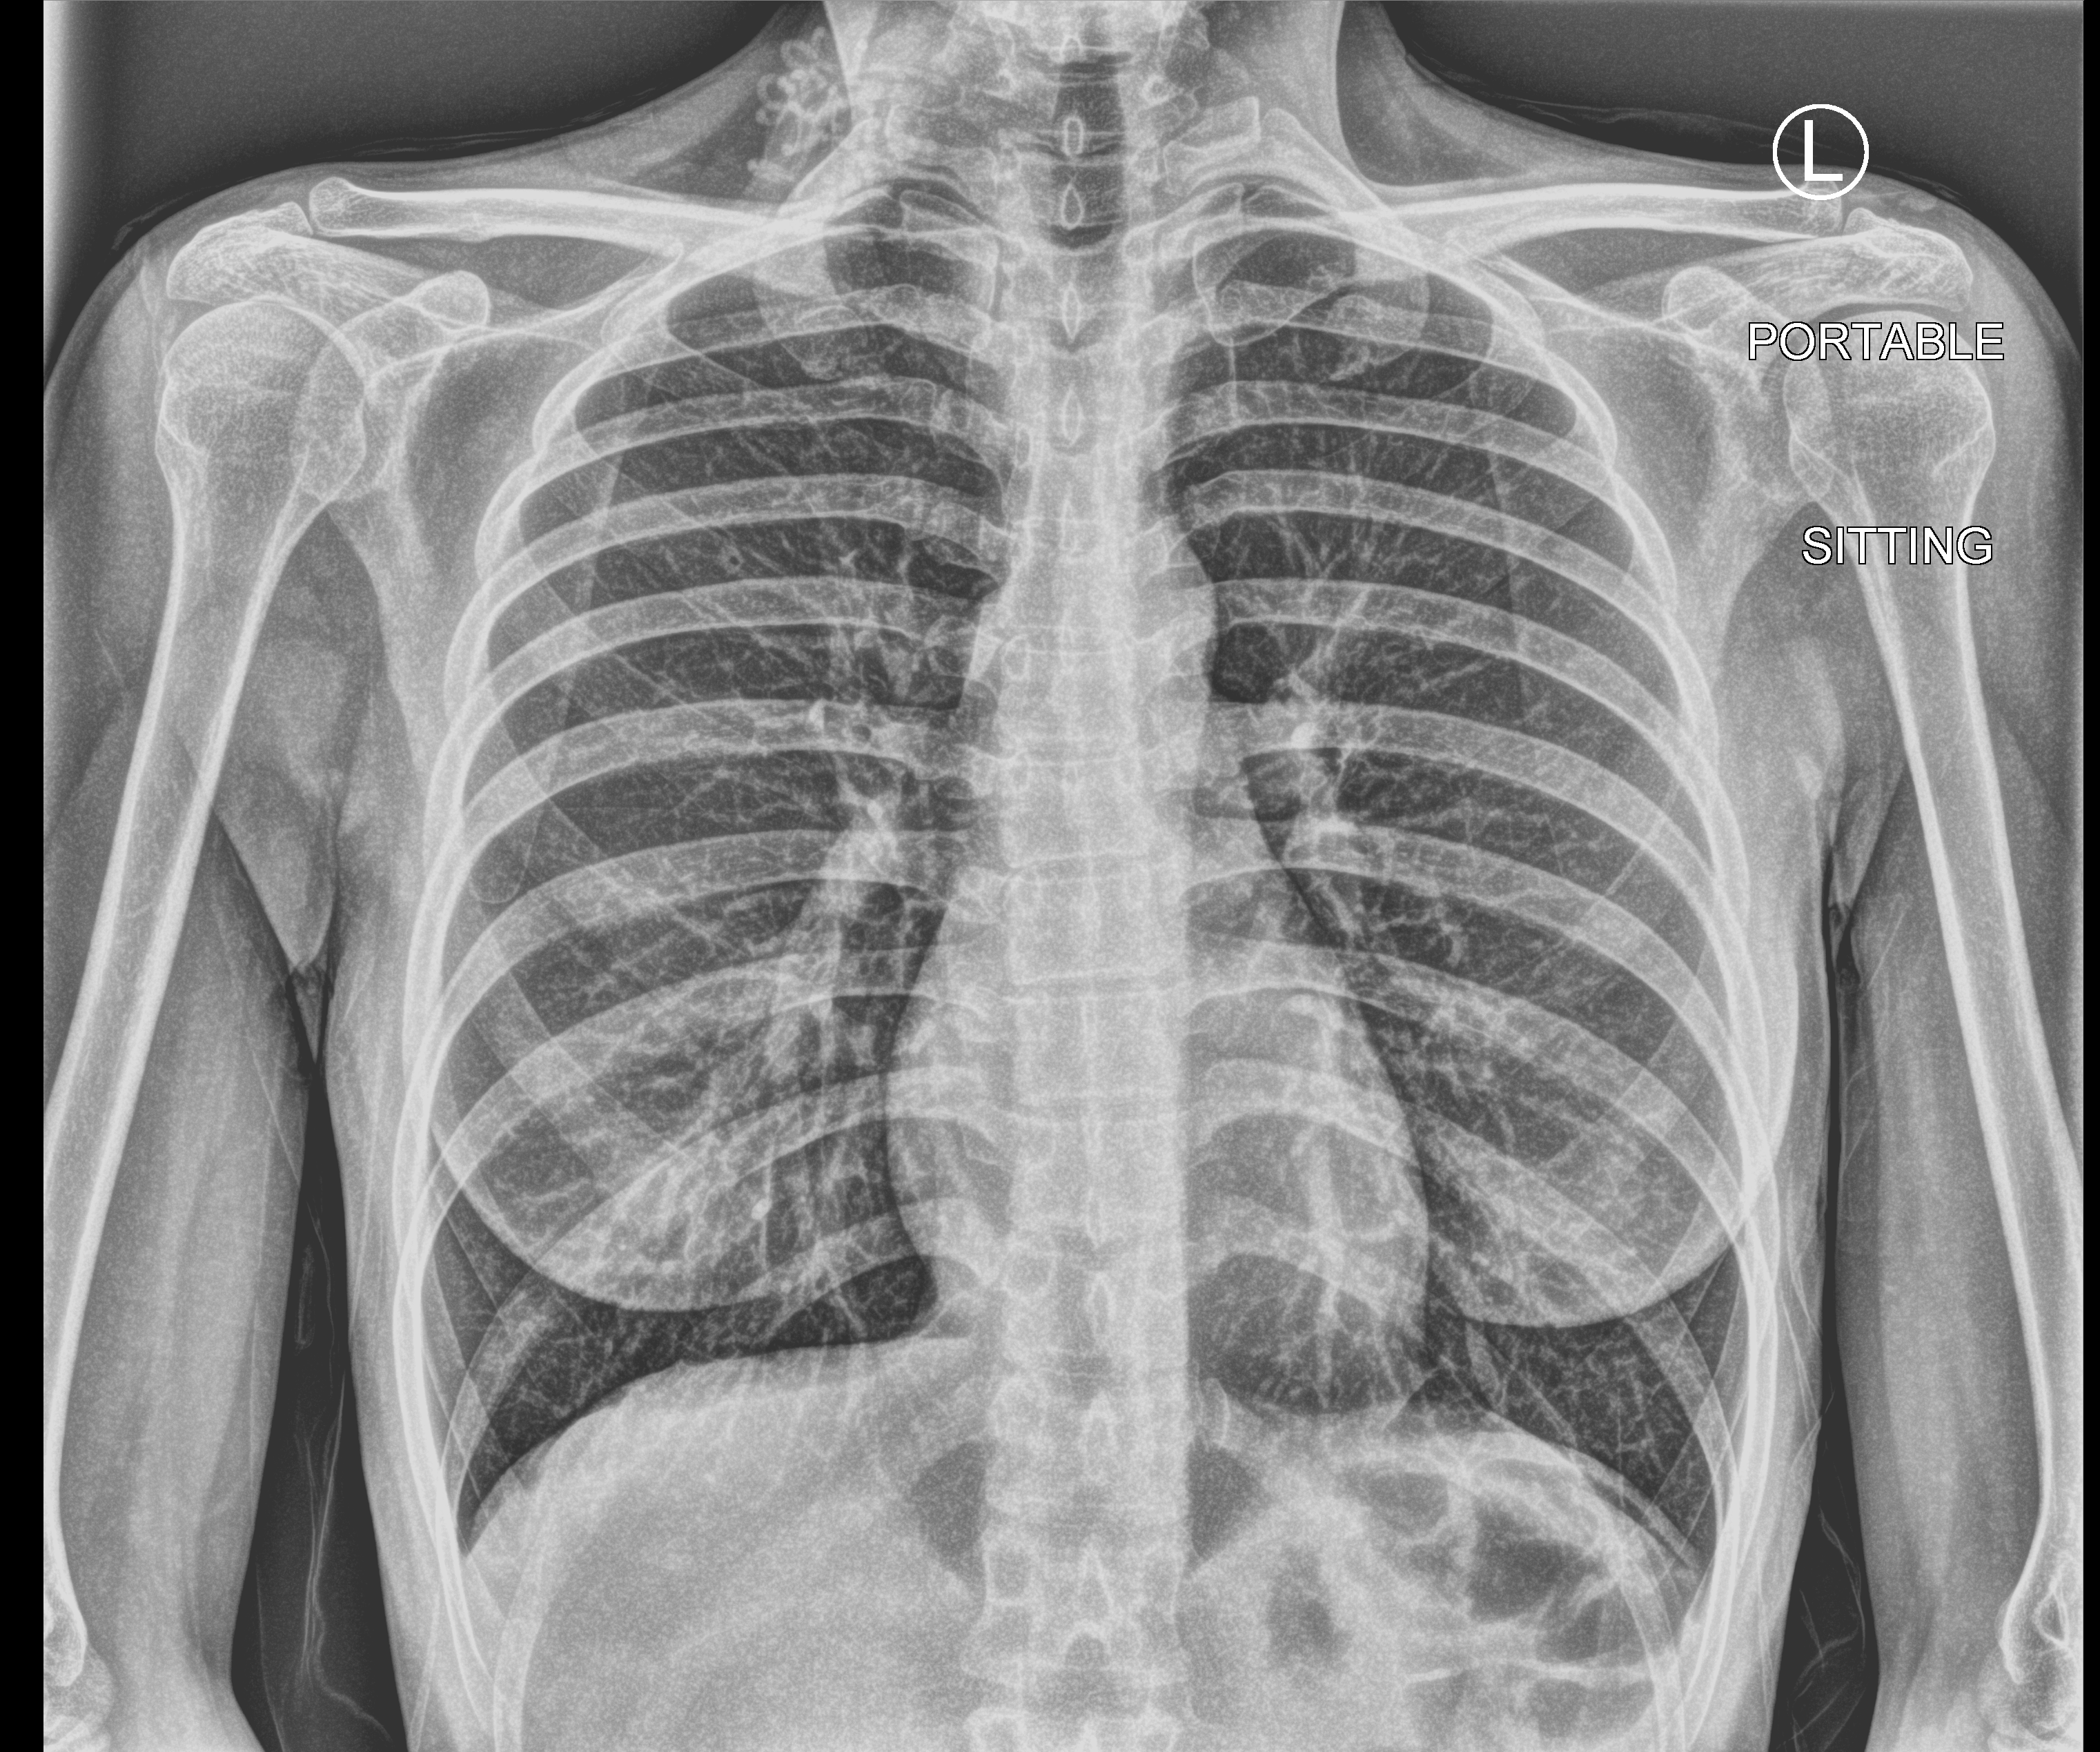
Portable chest radiograph; anteroposterior (AP) projection. Female patient hospitalised with COVID-19, age 18–59 years.
From the hospital-stay record, not from the radiograph (when in the stay this image was taken is not recorded): admitted to intensive care during this hospital stay: no.